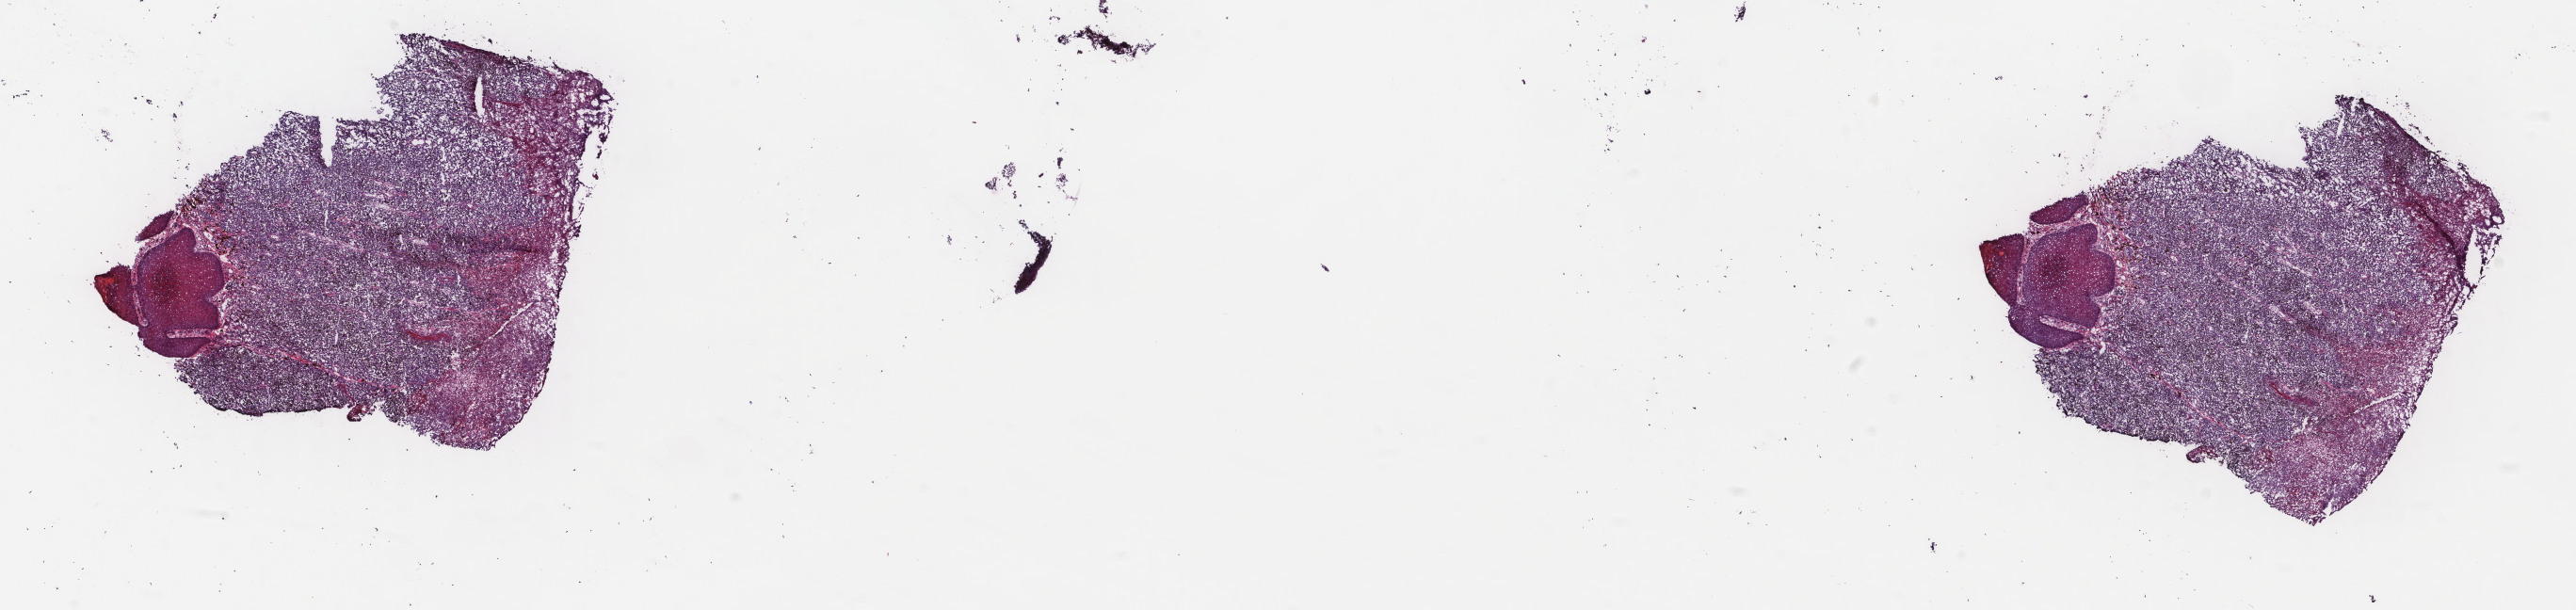
H&E whole-slide image — shown as a low-resolution overview of the whole scanned area (about 21.7 x 5.1 mm); frozen section from the top of the tissue portion; metastatic tumour sample. Male, age 85 years at initial diagnosis. Slide review estimates, as recorded: tumour cells 93%, tumour nuclei 92%, normal cells 7%, stromal cells 0%, necrosis 0%. Inflammatory infiltration, as recorded: lymphocyte infiltration 0%, monocyte infiltration 0%, neutrophil infiltration 0%.
This section: metastatic tumour tissue. Patient diagnosis: Malignant melanoma, NOS.